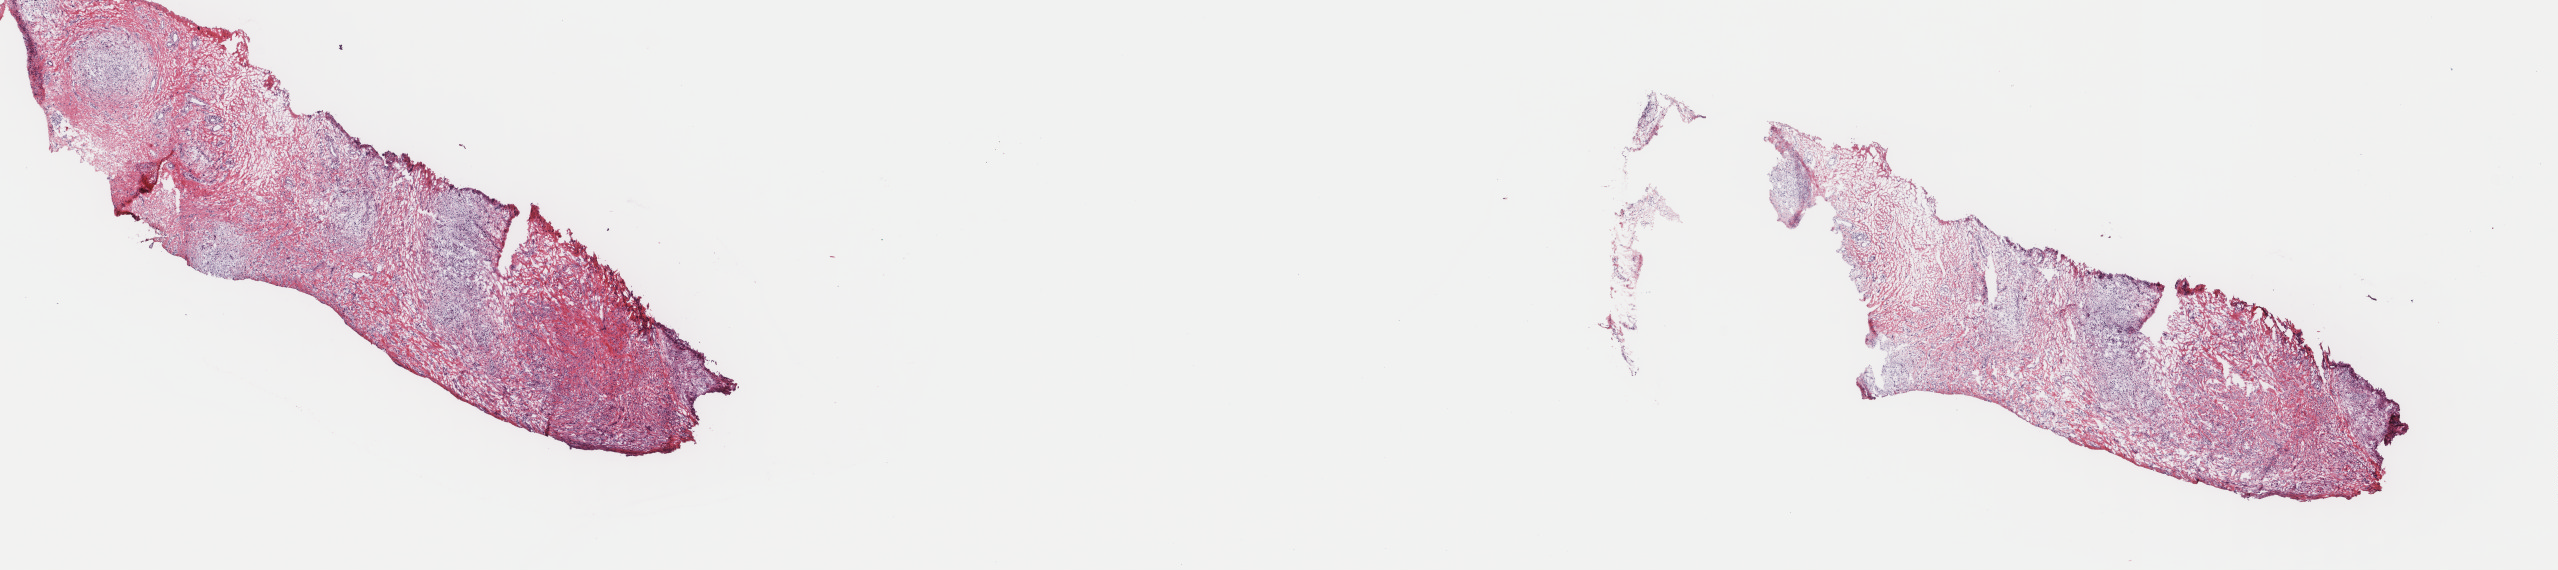
H&E-stained whole-slide image — whole scanned area (about 20.3 x 4.5 mm, slide scanned at 40x) shown as a low-resolution overview. Frozen section from the top of the tissue portion. Connective, subcutaneous and other soft tissues, primary tumour sample. Patient: female, age at initial diagnosis 55 years. Pathologist review of this section (percent, as recorded): tumour cells 40%, tumour nuclei 100%.
Diagnosis: Fibromyxosarcoma (connective, subcutaneous and other soft tissues of lower limb and hip).